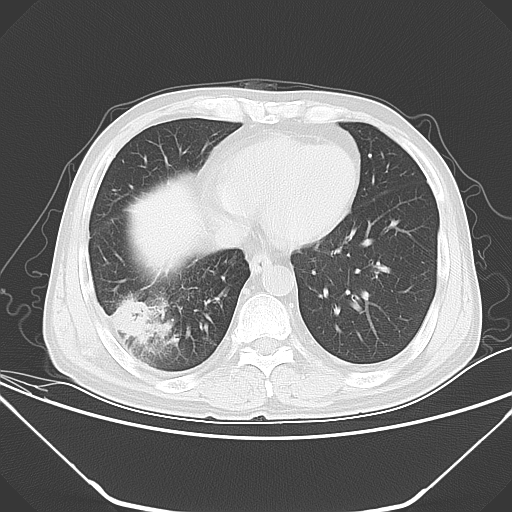
Chest CT, one axial slice. Slice 15 of 52 in the series (ordered by position). 120 kVp. Lung window (W 1500 / L -600 HU). 512 × 512 image matrix, field of view 379 × 379 mm. Patient: male, 54 years. Case-level facts recorded for this patient, not image findings: clinical TNM (as recorded): T2 N1 M0.
Structures marked on this image (rectangle marked by the reading radiologist):
- lung tumour (recorded histology: adenocarcinoma): bounding box (x1, y1, x2, y2) in pixels: (108, 299, 151, 338)